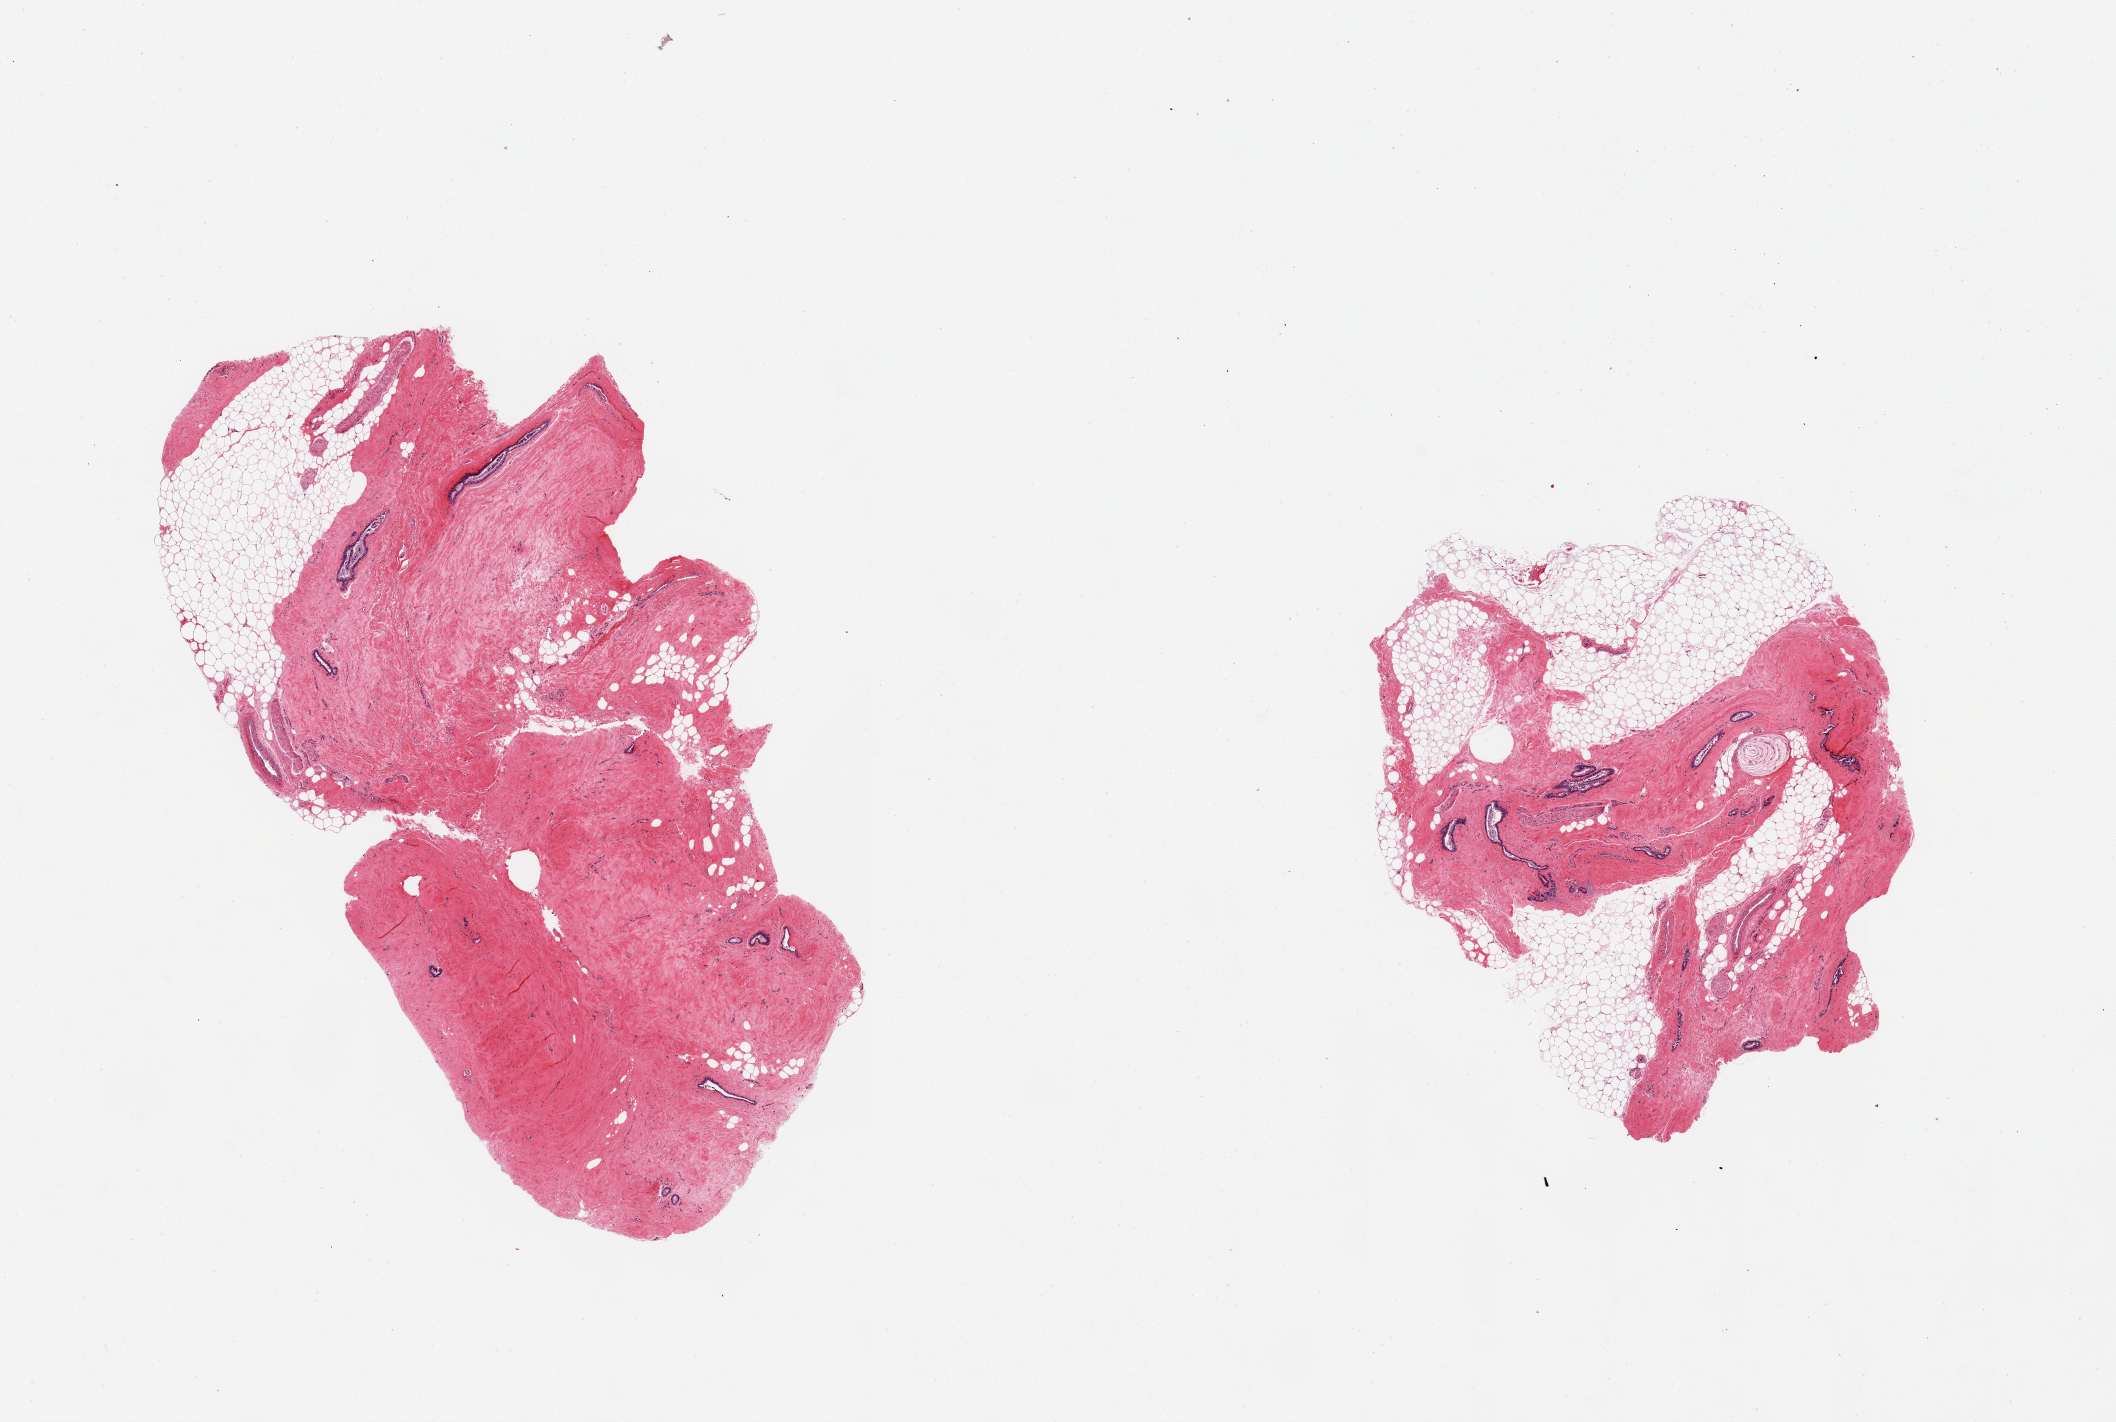
H&E whole-slide image, brightfield, shown as a low-resolution overview of the whole scanned area (about 16.7 x 11.2 mm); PAXgene-fixed paraffin-embedded (PFPE) section; section of breast (target tissue); donor tissue sample. Male donor.
Reviewer comment on this tissue sample: 2 pieces; gynecomastoid changes.